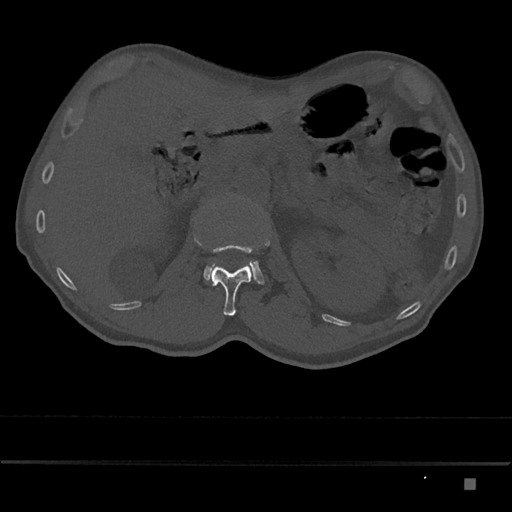
CT including the spine, one axial slice. Position 524 of 797 along the scan axis. Reconstruction kernel Br40s/3. Bone window (W 1800 / L 400 HU). 512 × 512 image matrix, field of view 390 × 390 mm. Male patient, age 72 years. Case-level facts recorded for this patient, not image findings: primary cancer: prostate.
Annotated regions visible in this slice (semi-automatic segmentation, software-assisted and operator-edited):
- L1 vertebra: bounding box (x1, y1, x2, y2) in pixels: (210, 240, 270, 316)
- L2 vertebra: (203, 261, 265, 285)